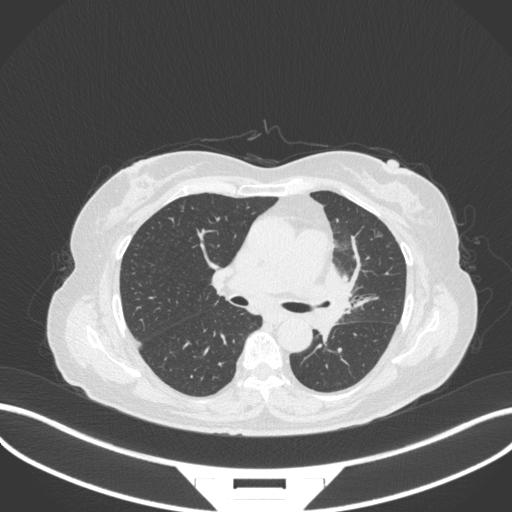
Chest CT, one axial slice; slice 195 of 382 in the series (ordered by position); reconstruction kernel B31f; 120 kVp; lung window (W 1500 / L -600 HU); 1 mm slice thickness; 512 × 512 image matrix. Patient: female, 64 years. Case-level facts recorded for this patient, not image findings: clinical TNM (as recorded): T2a N2 M0.
Outlined on this slice (rectangle marked by the reading radiologist):
- lung tumour (recorded histology: adenocarcinoma): box from (x=323, y=258) to (x=358, y=337) px